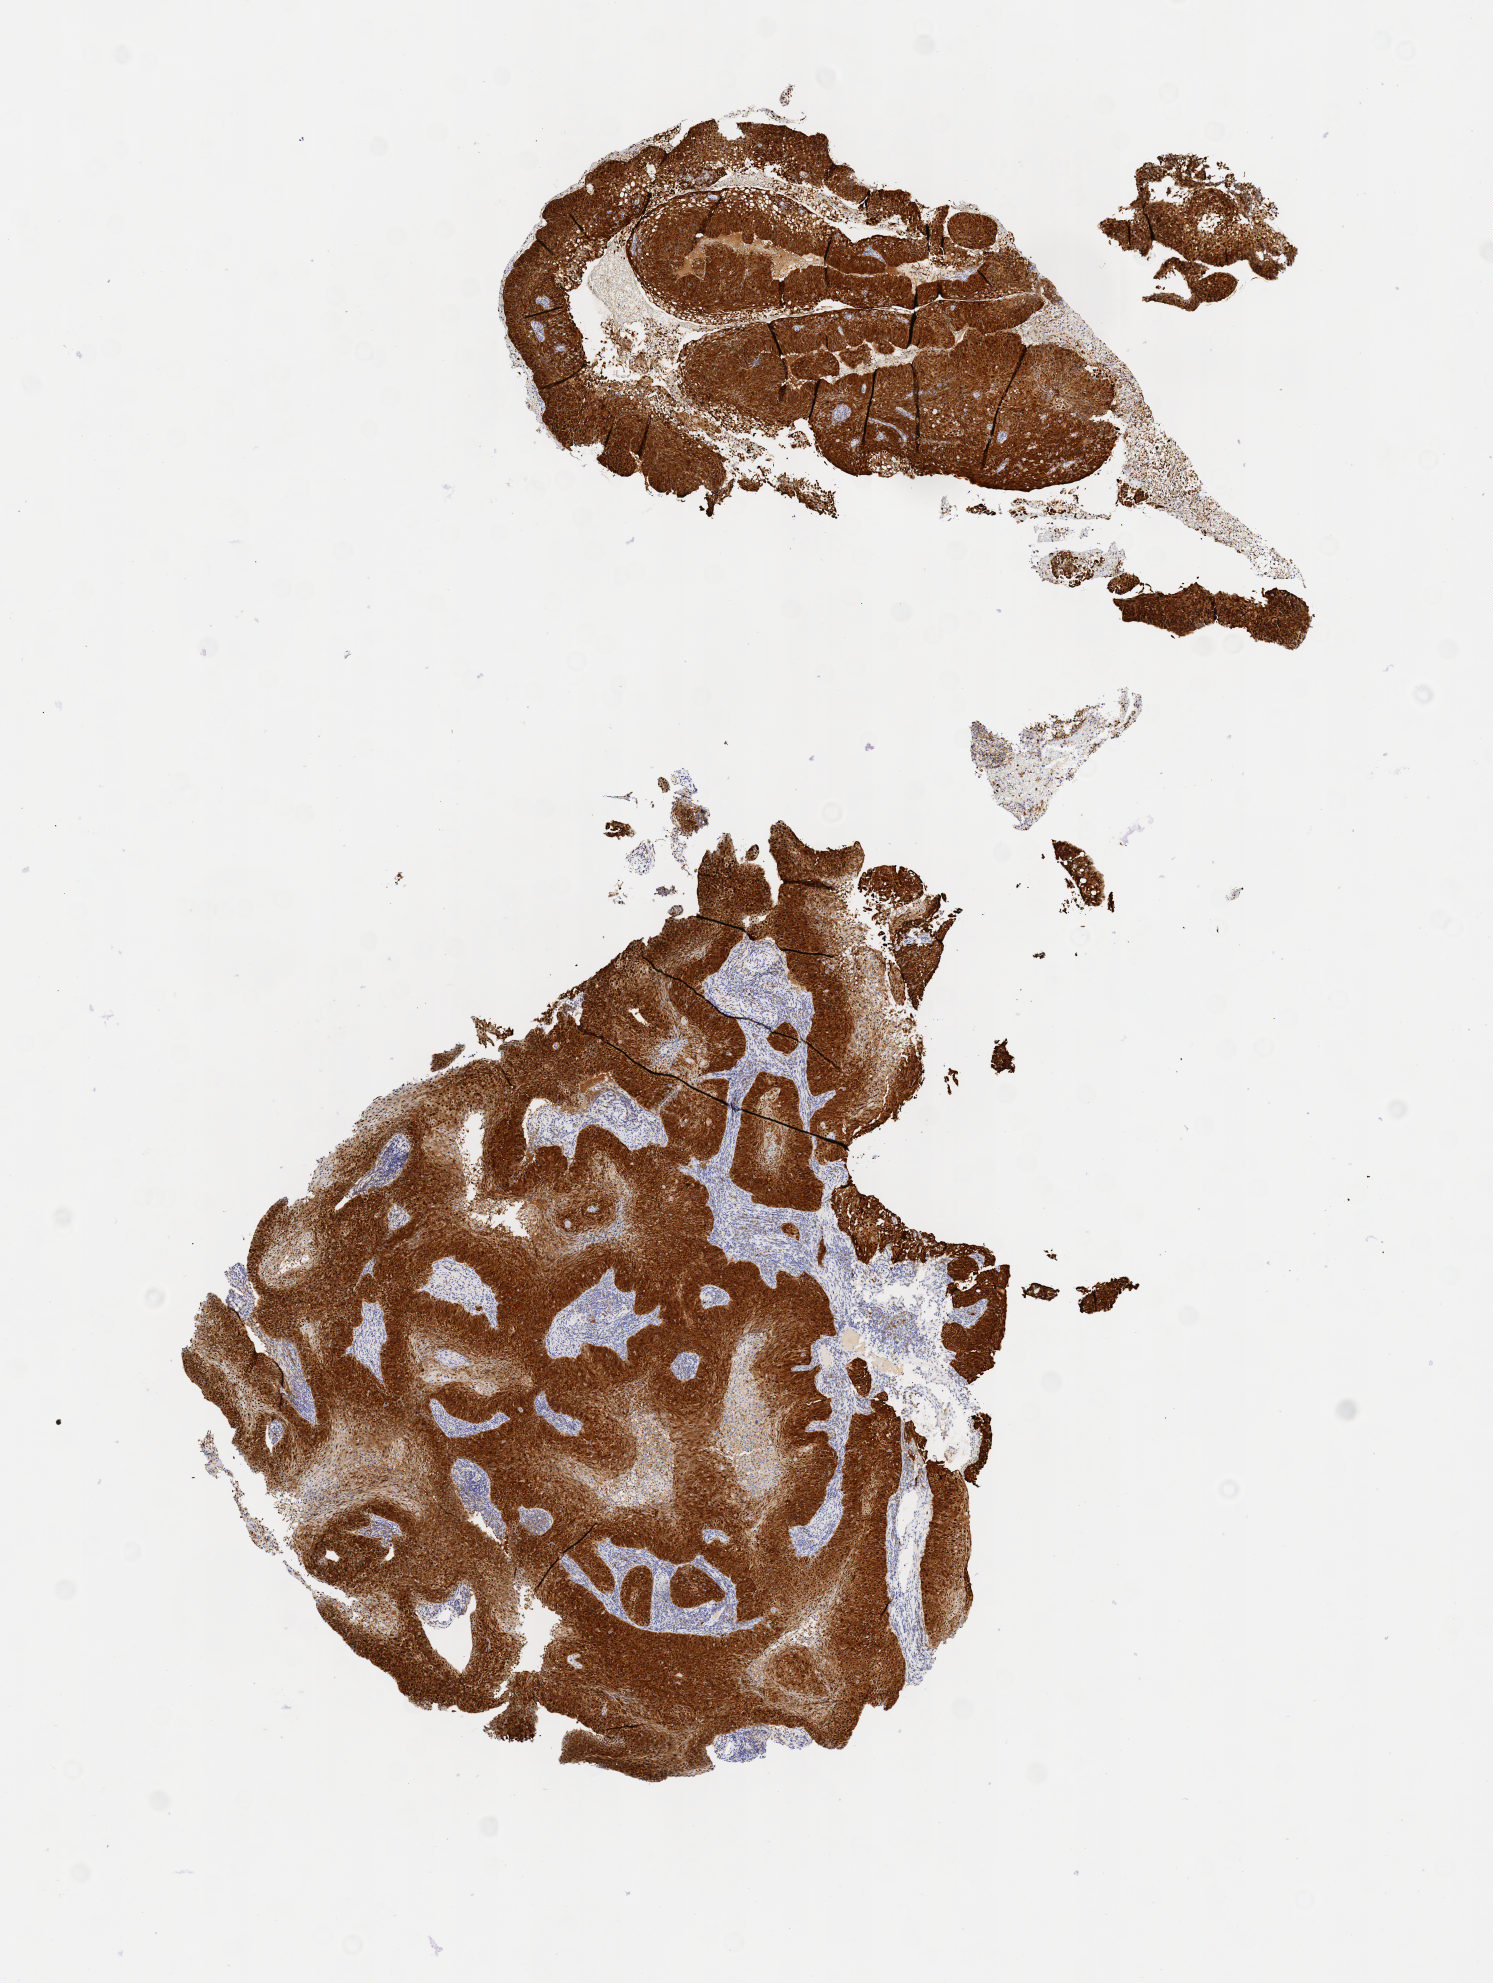
Whole-slide image, immunohistochemical stain for p16 (p16INK4a), a low-resolution overview of the entire scanned area, about 6.0 x 8.0 mm; tumor tissue; anatomic site: cervix. Patient: female, aged 54.
Histologic diagnosis: Squamous cell carcinoma, large cell, nonkeratinizing, NOS.